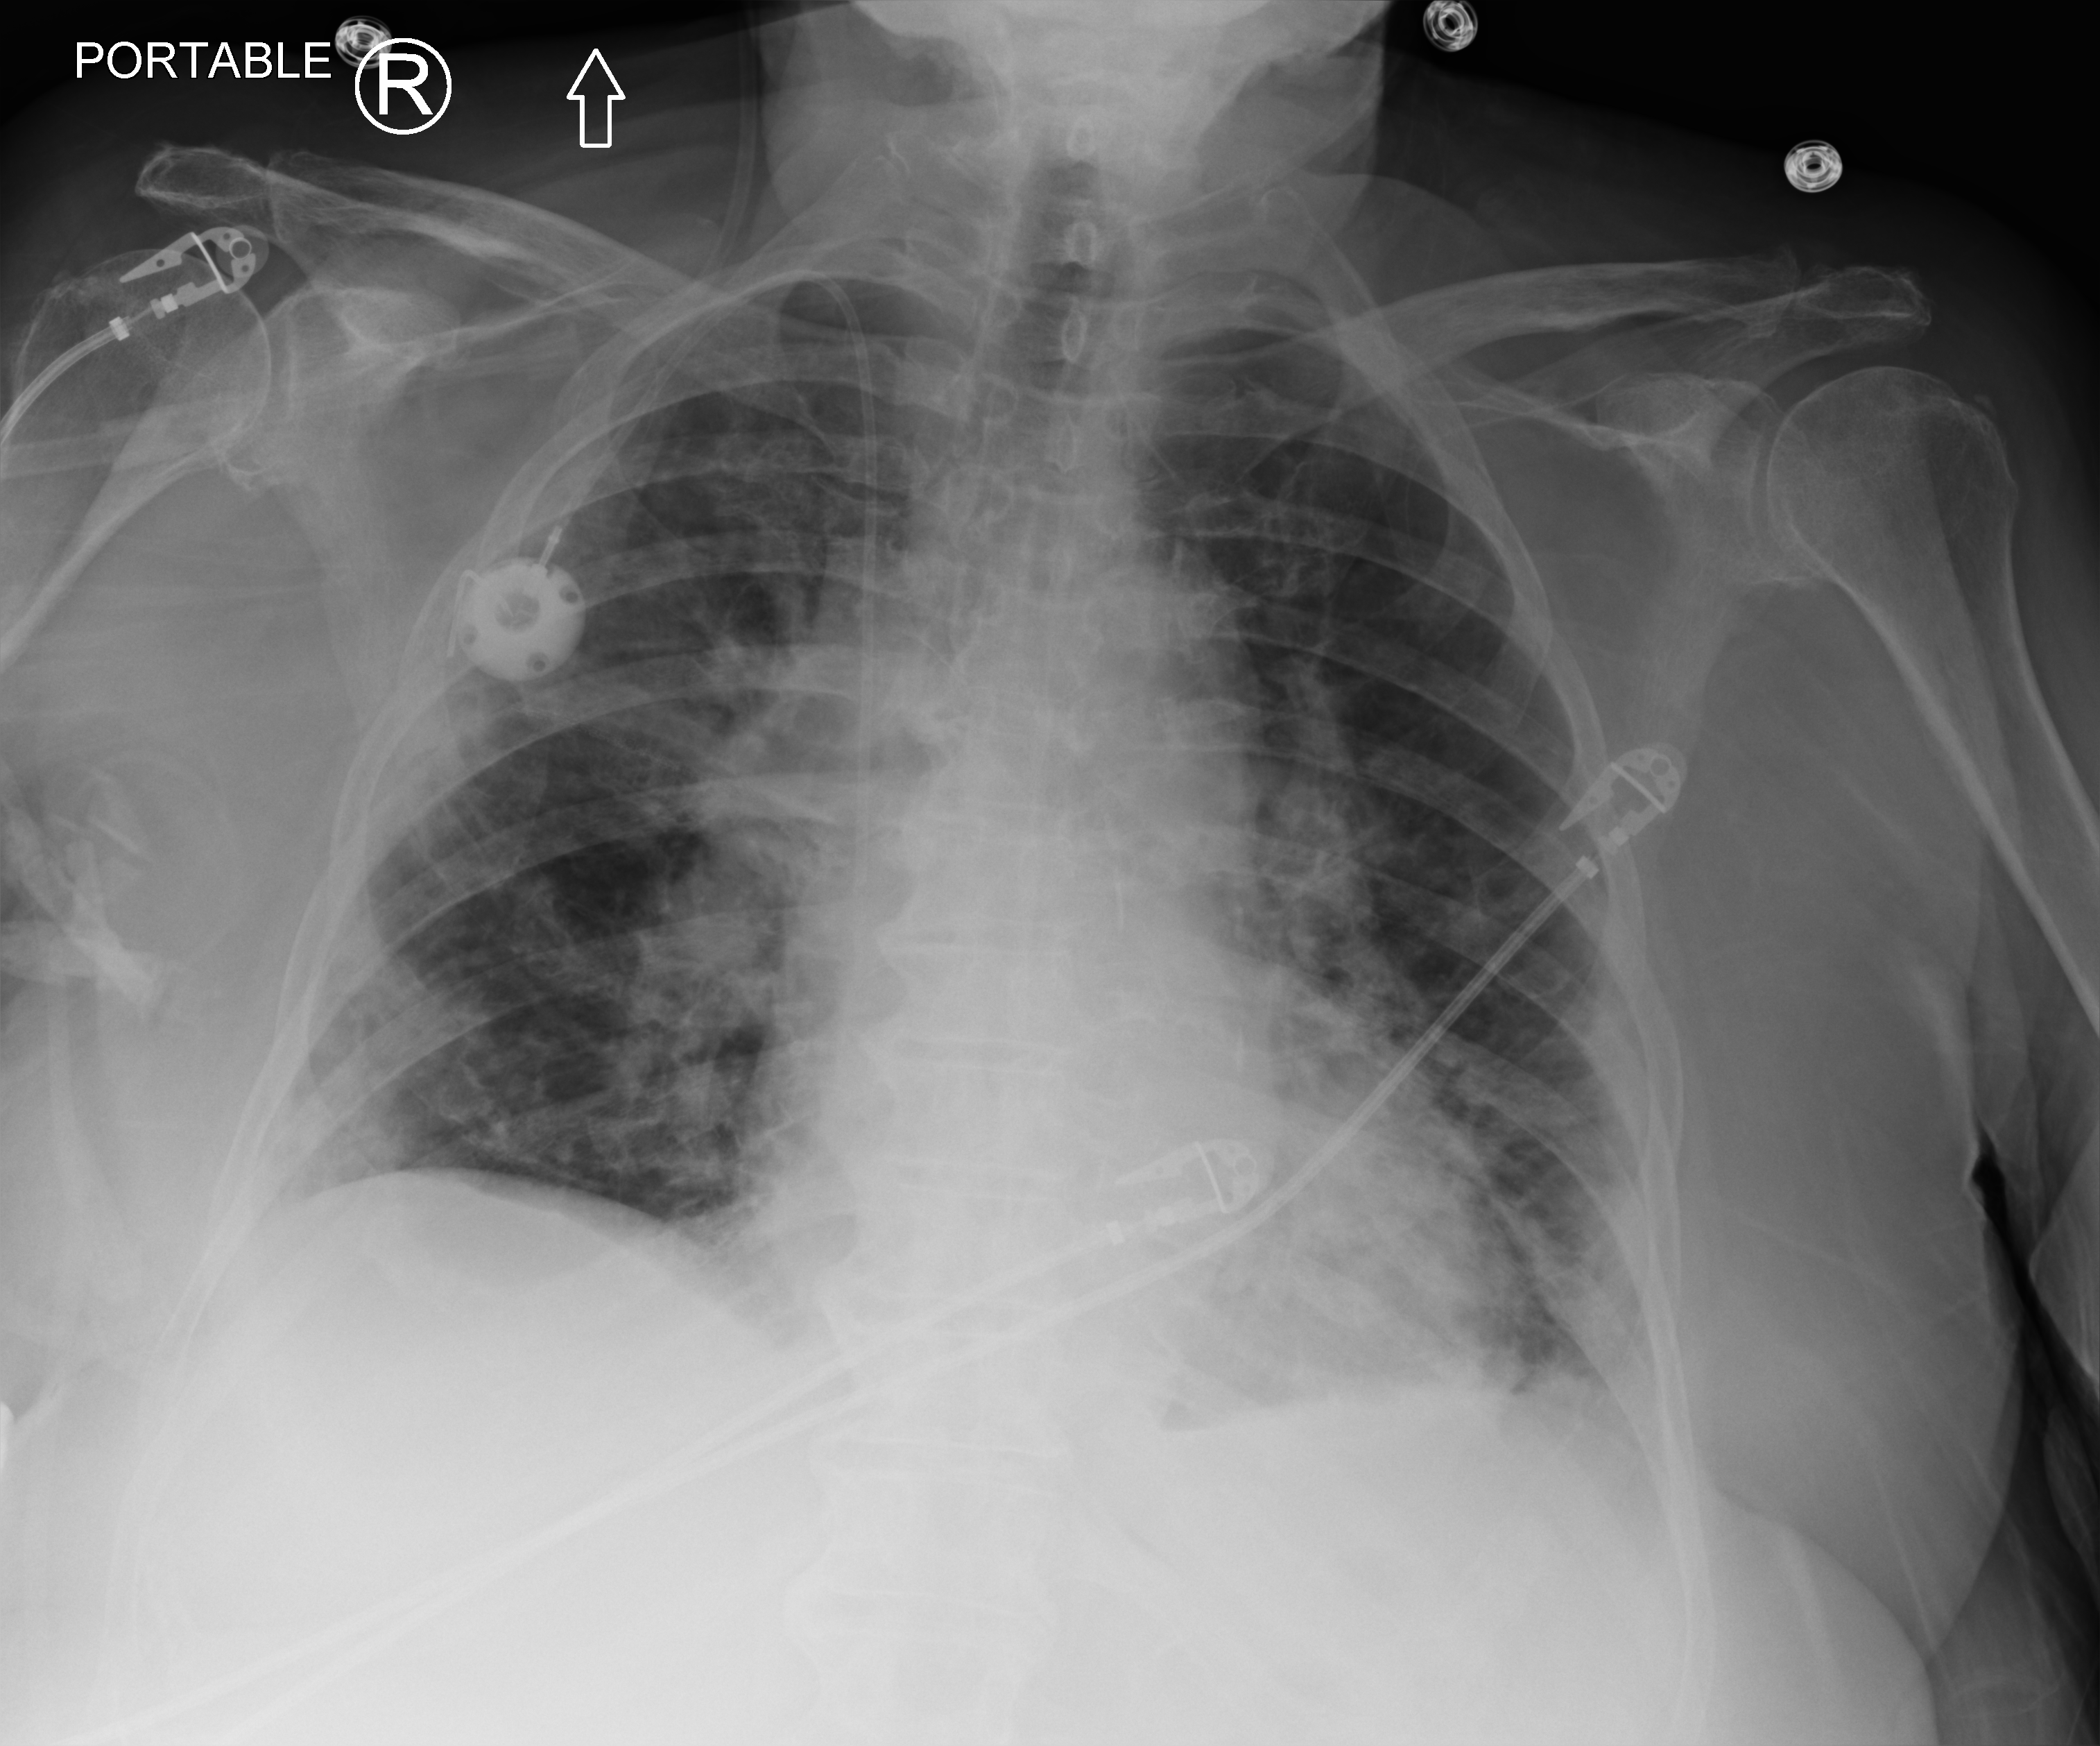
Bedside chest radiograph (computed radiography); anteroposterior (AP) projection. Patient hospitalised with COVID-19; female, aged 75–90 years.
From the hospital-stay record, not from the radiograph (when in the stay this image was taken is not recorded): mechanically ventilated during this hospital stay: no.